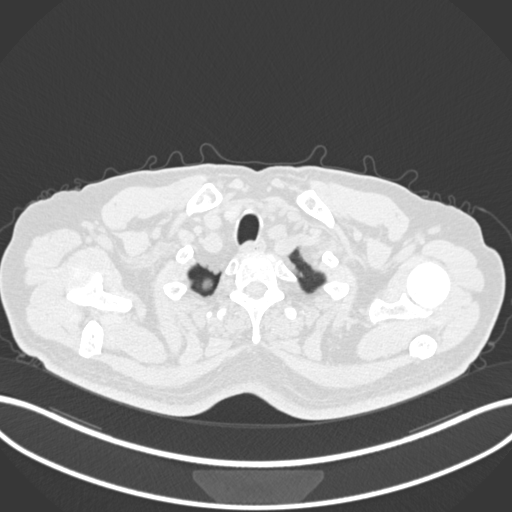
Chest CT, one axial slice; slice 205 of 218 in the series (ordered by position); reconstruction kernel B30f; lung window (W 1500 / L -600 HU); 512 × 512 image matrix. Male patient, age 68 years. From the clinical record (not read from this slice): clinical TNM (as recorded): T2a N0 M0.
Annotated regions visible in this slice (rectangle marked by the reading radiologist):
- lung tumour (recorded histology: adenocarcinoma): bounding box (x1, y1, x2, y2) in pixels: (201, 275, 215, 291)